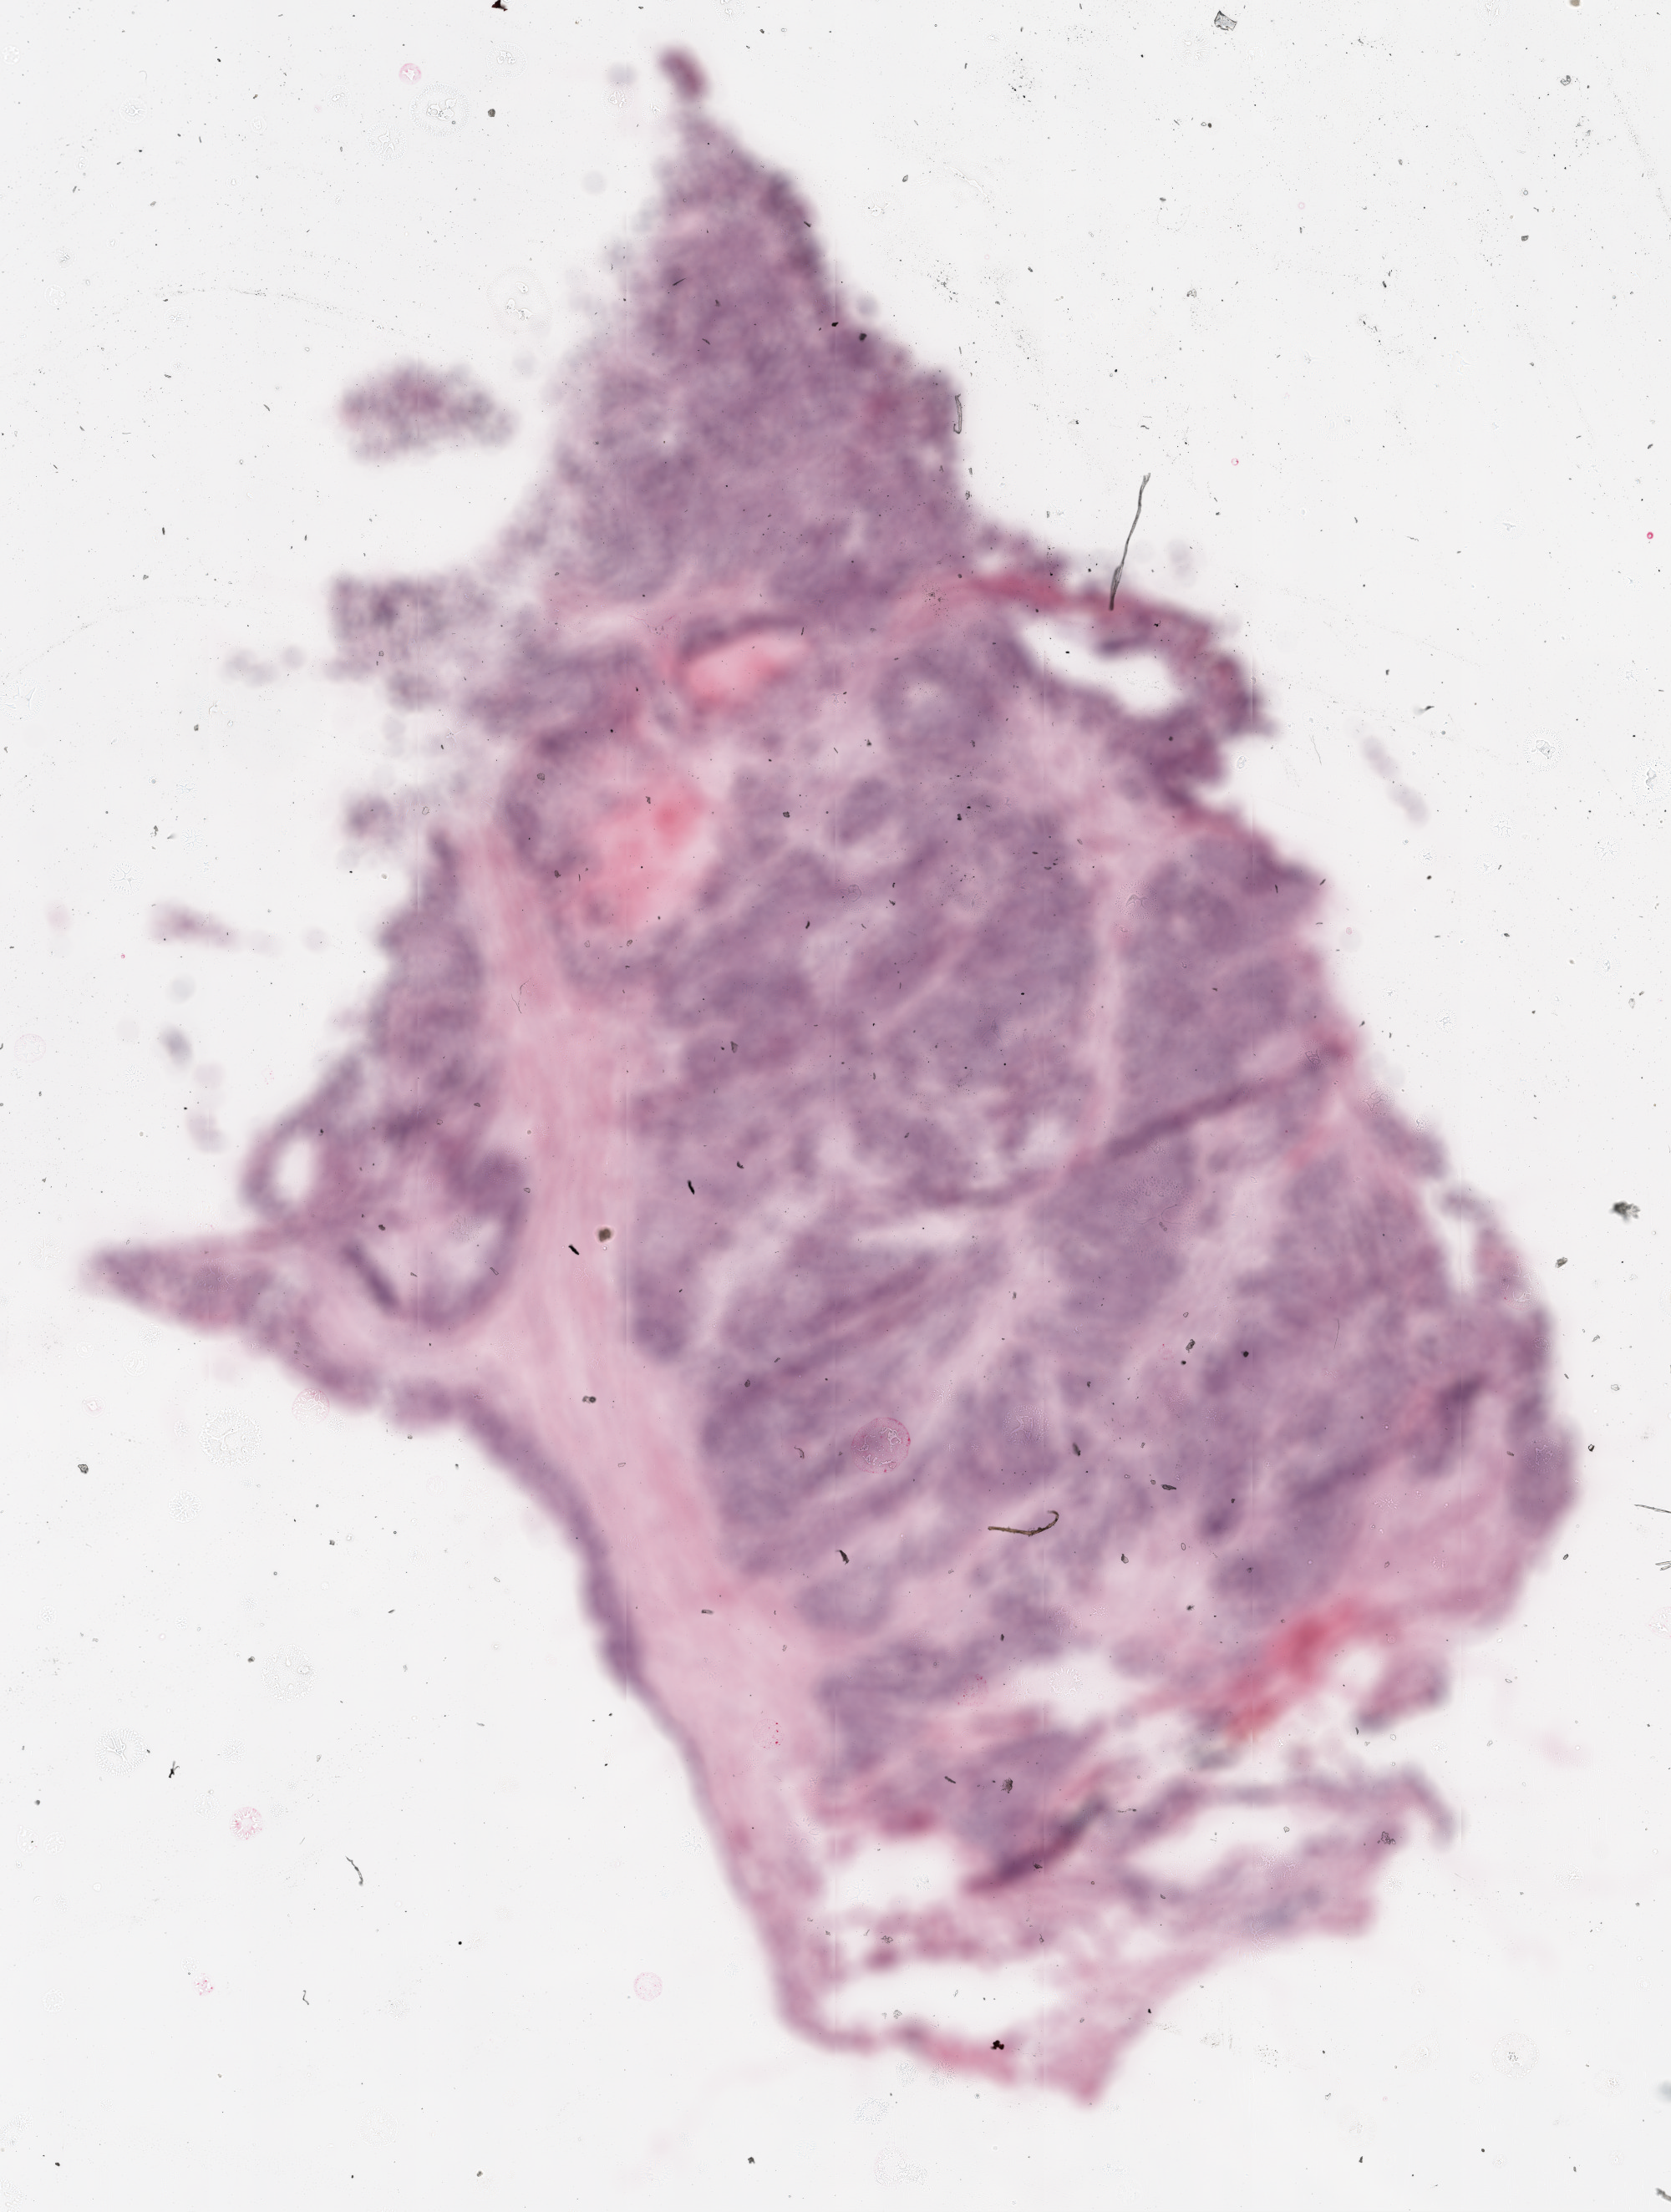
Hematoxylin and eosin (H&E) stained whole-slide image, shown as a low-resolution overview of the whole scanned area (about 8.0 x 10.6 mm); frozen section; ovary, primary tumour sample. Female, age 61 years at initial diagnosis. Histologic grade: G3 (poorly differentiated). Pathologist review of this section (percent, as recorded): tumour cells 80%, tumour nuclei 90%, normal cells 0%, stromal cells 20%, necrosis 0%.
Histologic diagnosis: Serous cystadenocarcinoma, NOS. Laterality: bilateral. FIGO stage: IIIC.